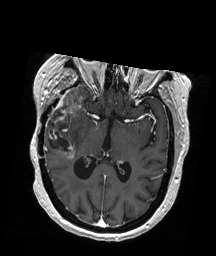
Brain MRI from a brain-tumour surgery series, one axial slice; position 106 of 192 along the scan axis; T1-weighted post-contrast; 1 mm slice thickness; 216 × 256 image matrix, field of view 211 × 250 mm. From the clinical record (not read from this slice): histopathology: Glioblastoma; WHO grade: 4; IDH mutation: no.
Annotated regions visible in this slice (outlined manually by an expert reader):
- tumour: bounding box (x1, y1, x2, y2) in pixels: (49, 86, 87, 158)